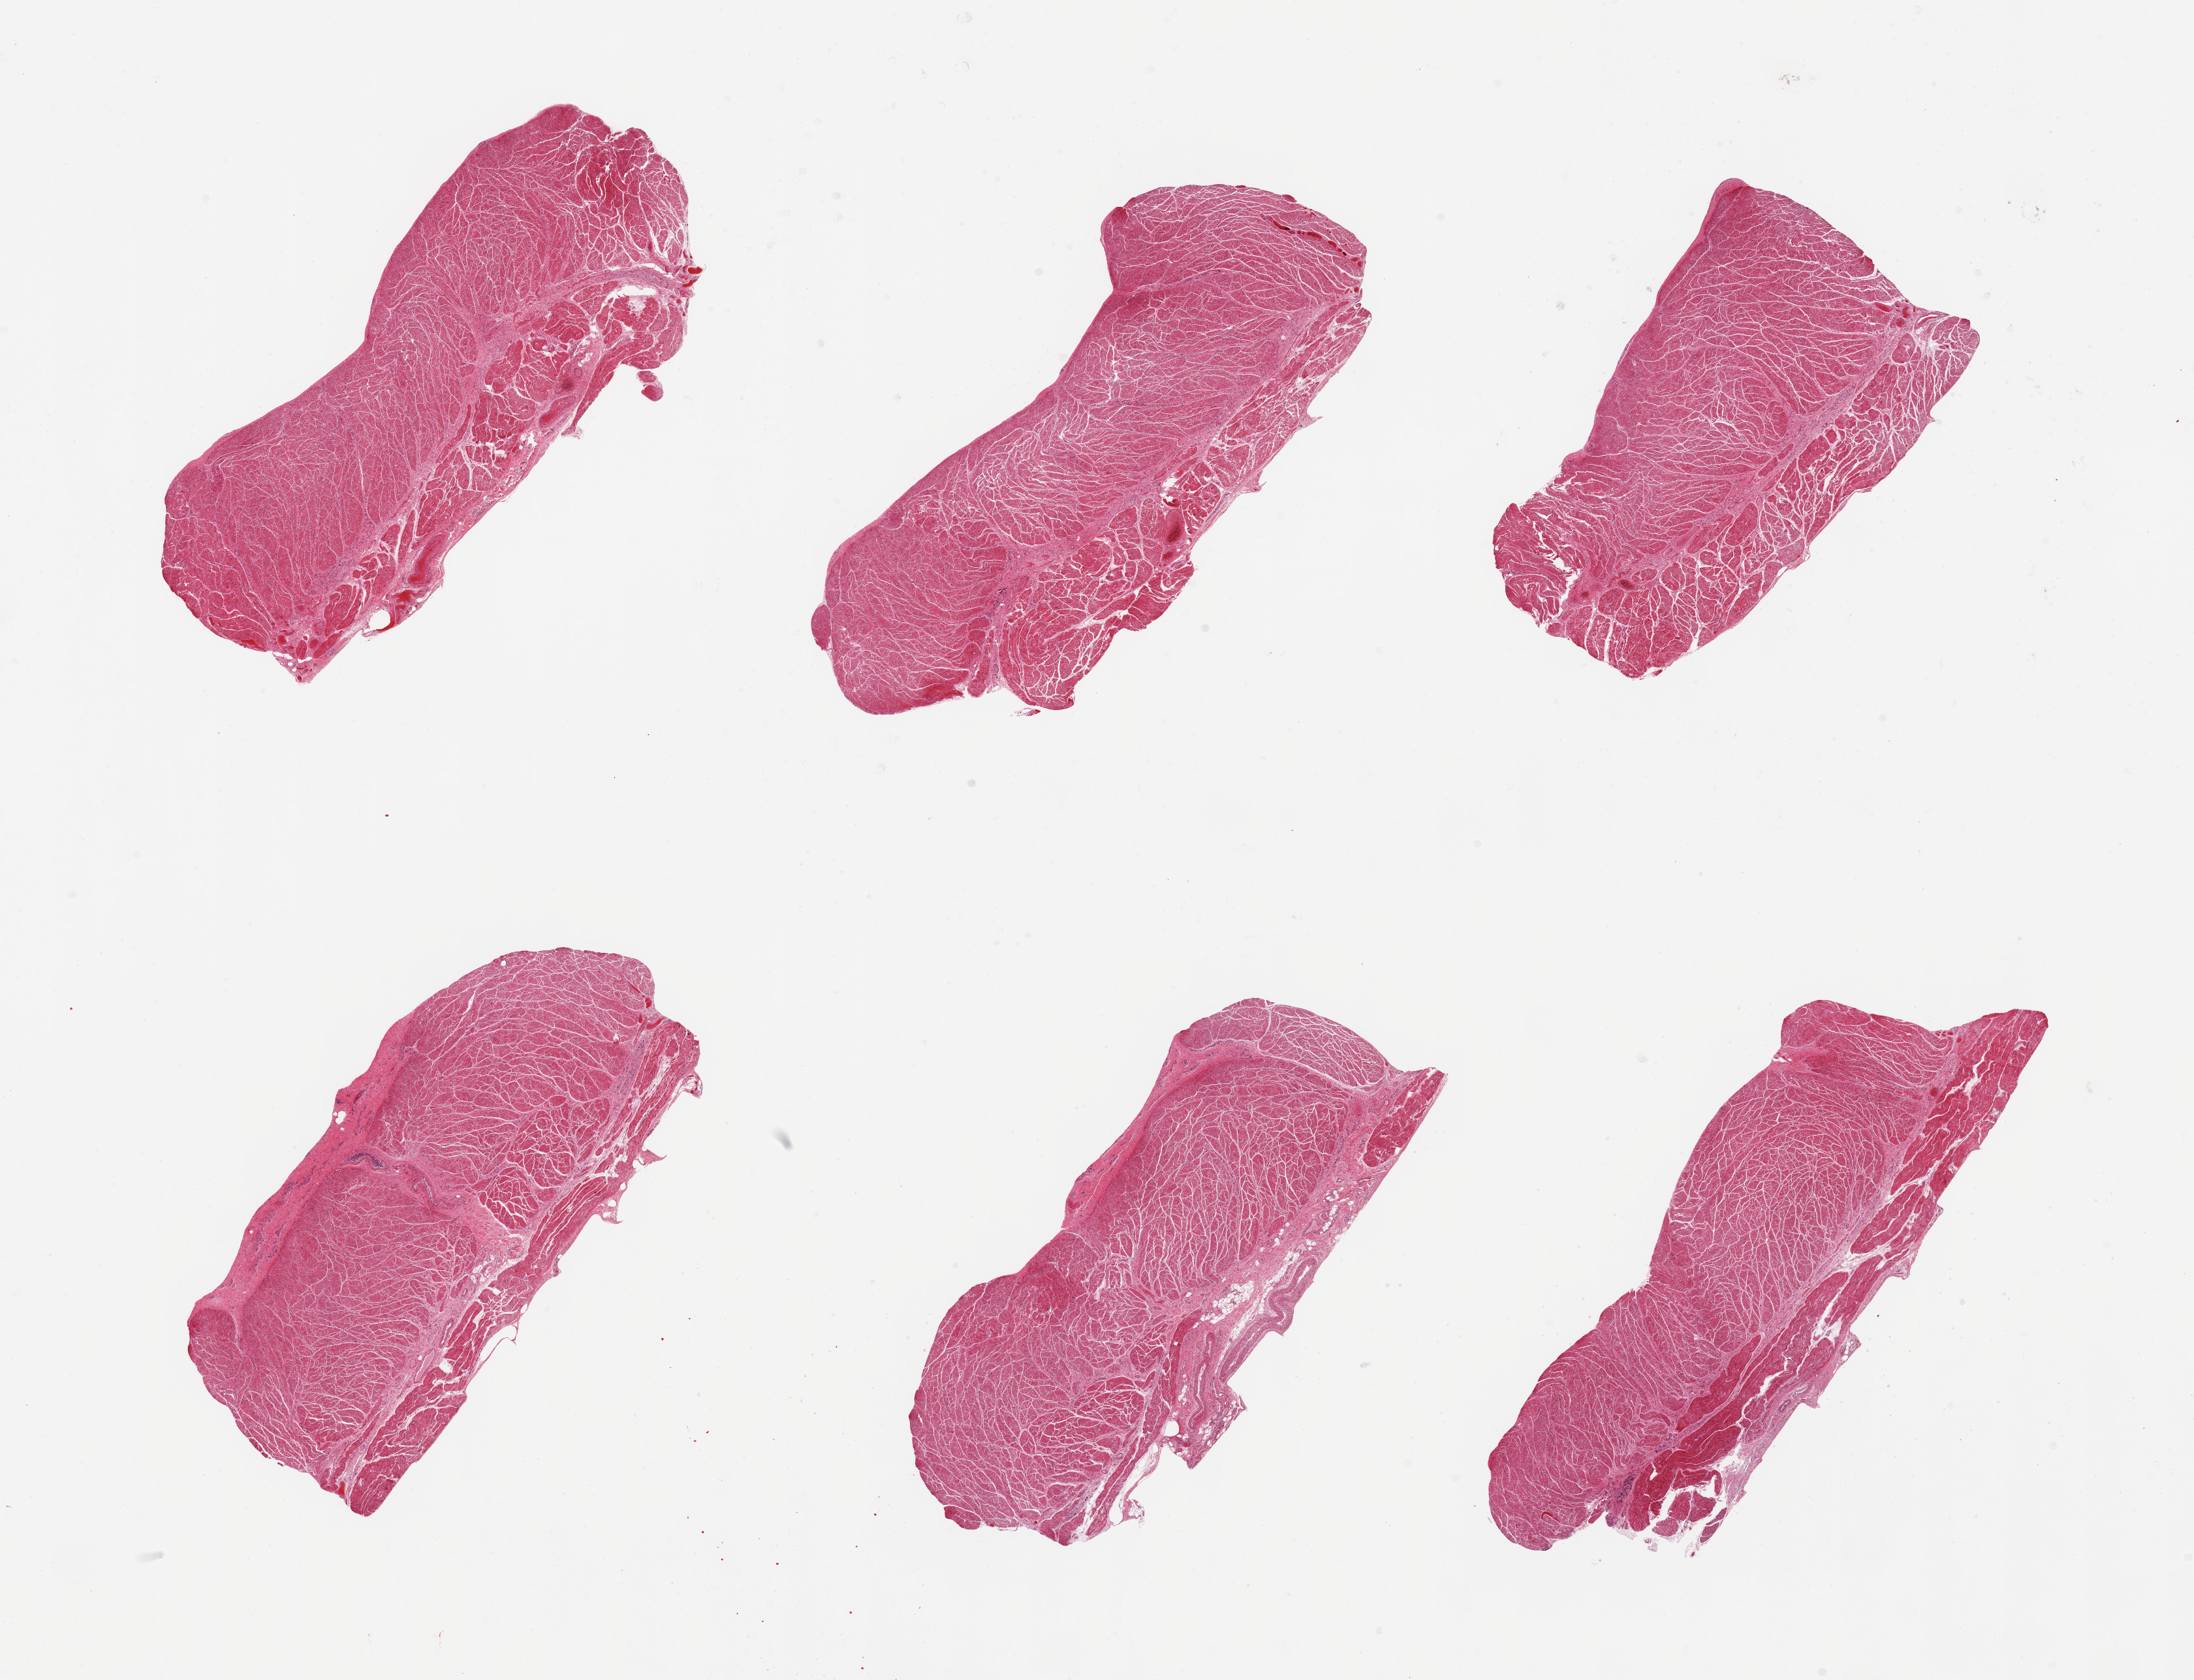
Whole-slide image, hematoxylin and eosin (H&E) stain — a low-resolution overview of the entire scanned area, about 26.6 x 20.4 mm, PAXgene-fixed paraffin-embedded (PFPE) section, sampled site (target tissue): esophageal muscle, tissue donor sample.
* review note (as recorded): 6 pieces, confirmed target muscularis